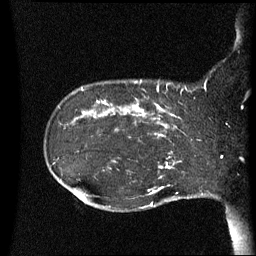
Breast MRI (dynamic contrast-enhanced), one sagittal slice. Slice 17 of 60 in the series (ordered by position). Dynamic contrast-enhanced series, image 2 of 3 at this slice position (ordered by acquisition). 1.5 T. TE 4.2 ms, TR 8.4 ms. 2.5 mm slice thickness. 256 × 256 image matrix, field of view 220 × 220 mm. Patient: female, 41 years. From the clinical record (not read from this slice): setting: breast cancer imaged before/during neoadjuvant chemotherapy; receptor status: HER2-positive.
Outlined on this slice (semi-automatically segmented with operator editing):
- analysis volume of interest (the breast-tissue region the enhancement analysis was run in; not a lesion): bounding box <122,84,195,137> (left, top, right, bottom; pixels)
- tumour enhancement mask (voxels above the 70 % enhancement threshold inside the analysis volume of interest): <132,86,179,137>